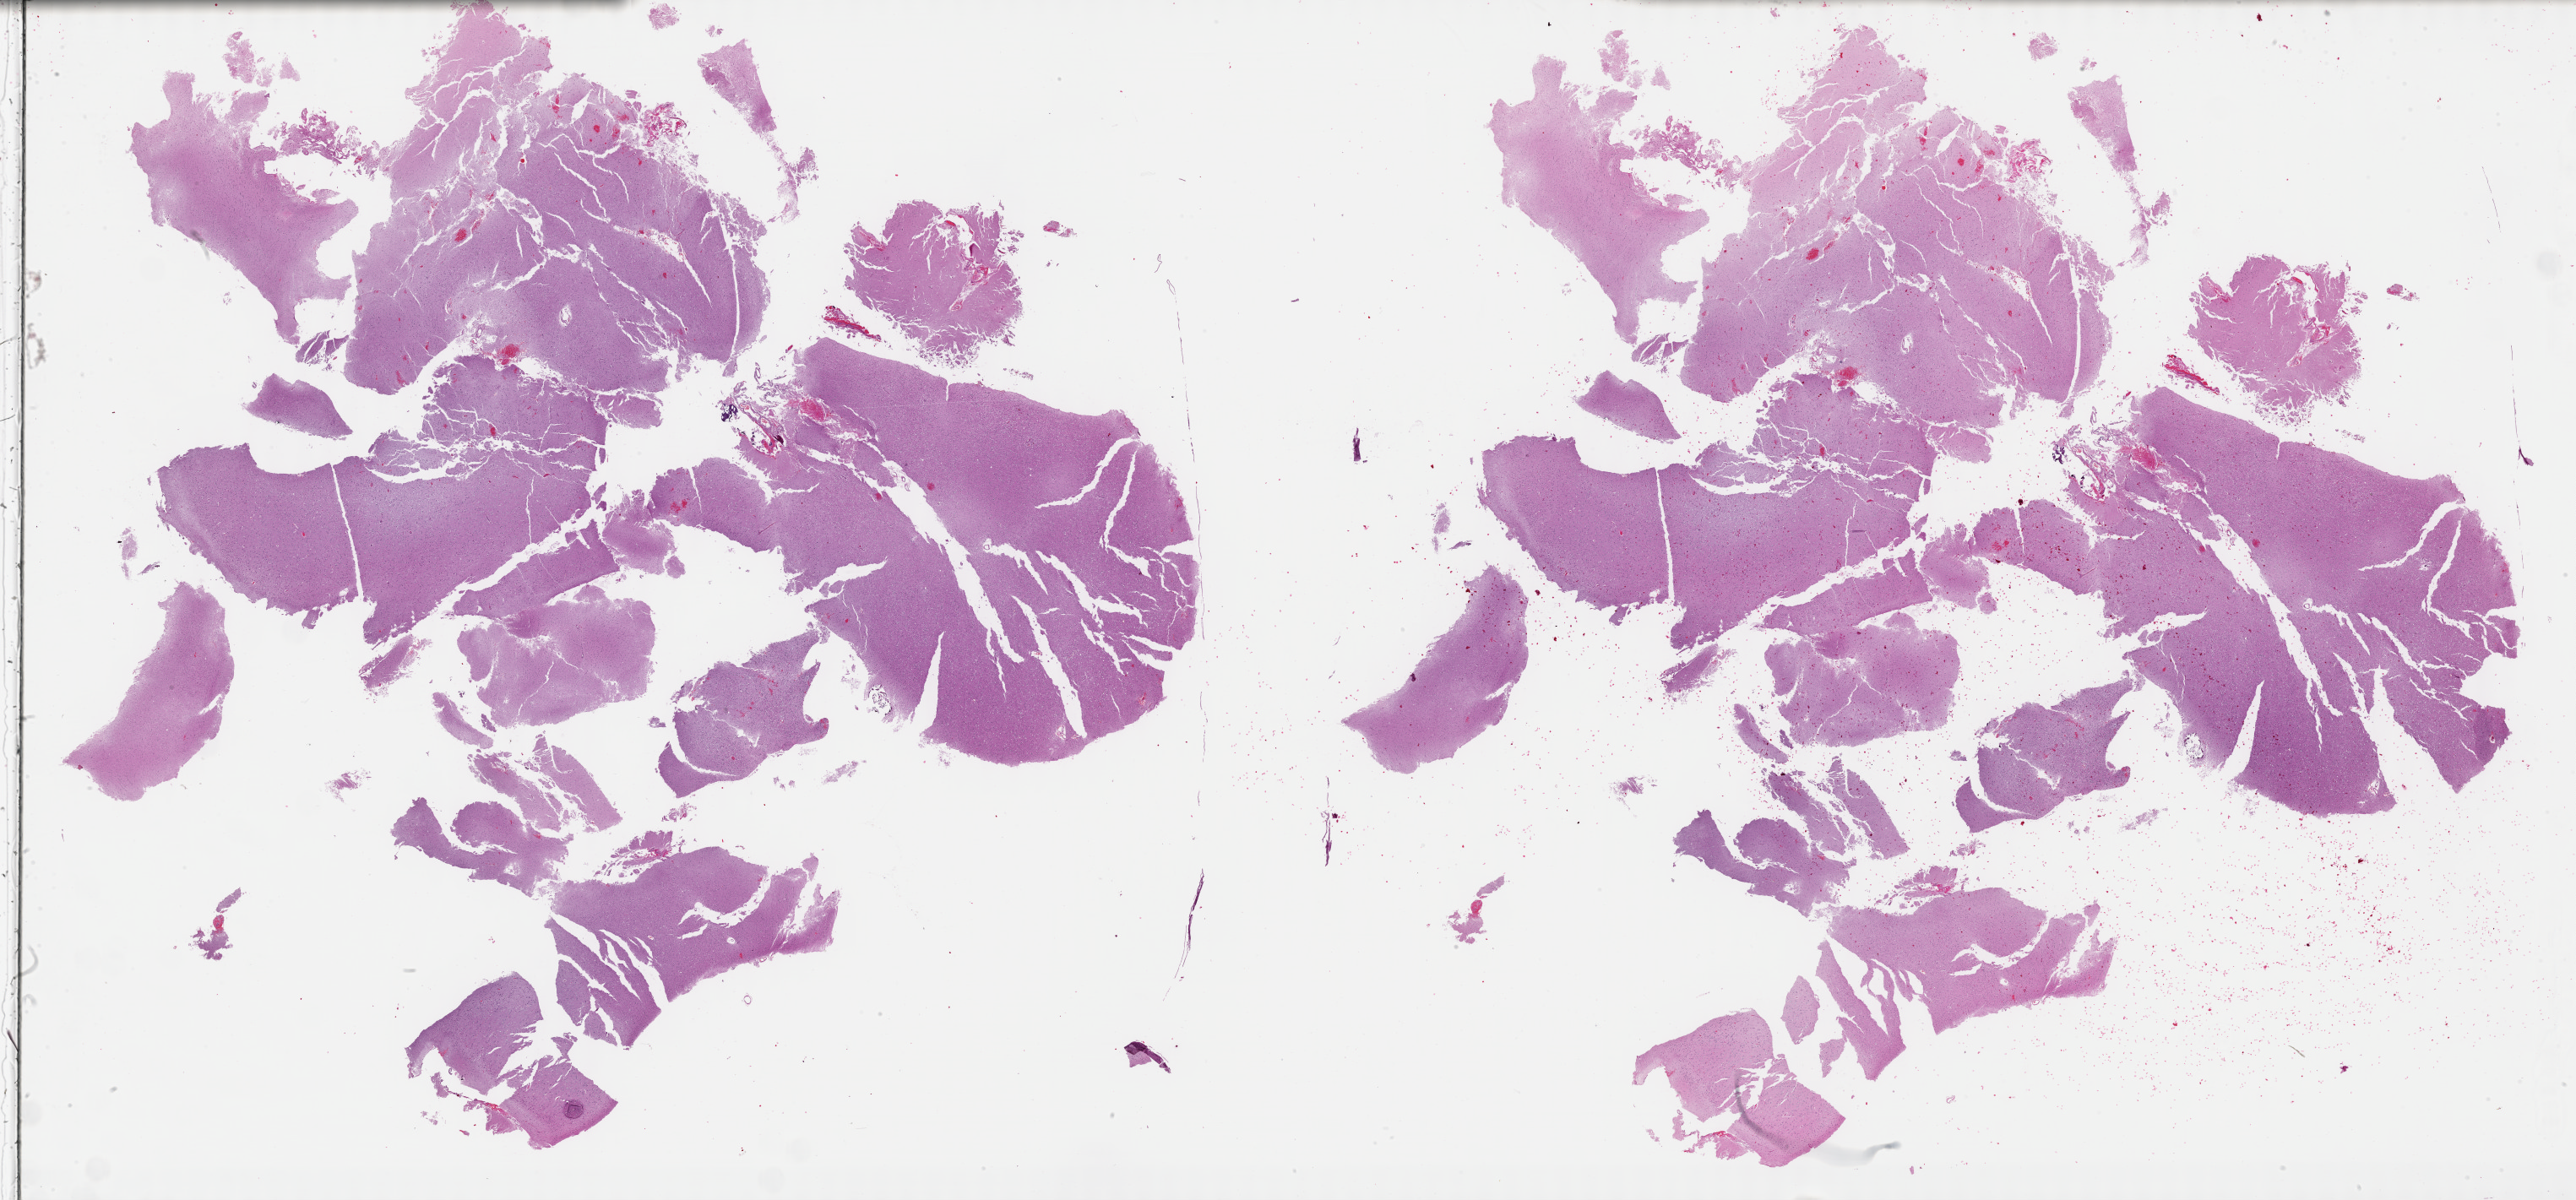
Digitized H&E tissue section (whole slide), a low-resolution overview of the entire scanned area, about 49.3 x 23.0 mm; formalin-fixed paraffin-embedded (FFPE) diagnostic section; primary tumour sample from the brain. Female, age 74 years at initial diagnosis. Histologic grade: G2 (moderately differentiated).
Histologic diagnosis: Mixed glioma.